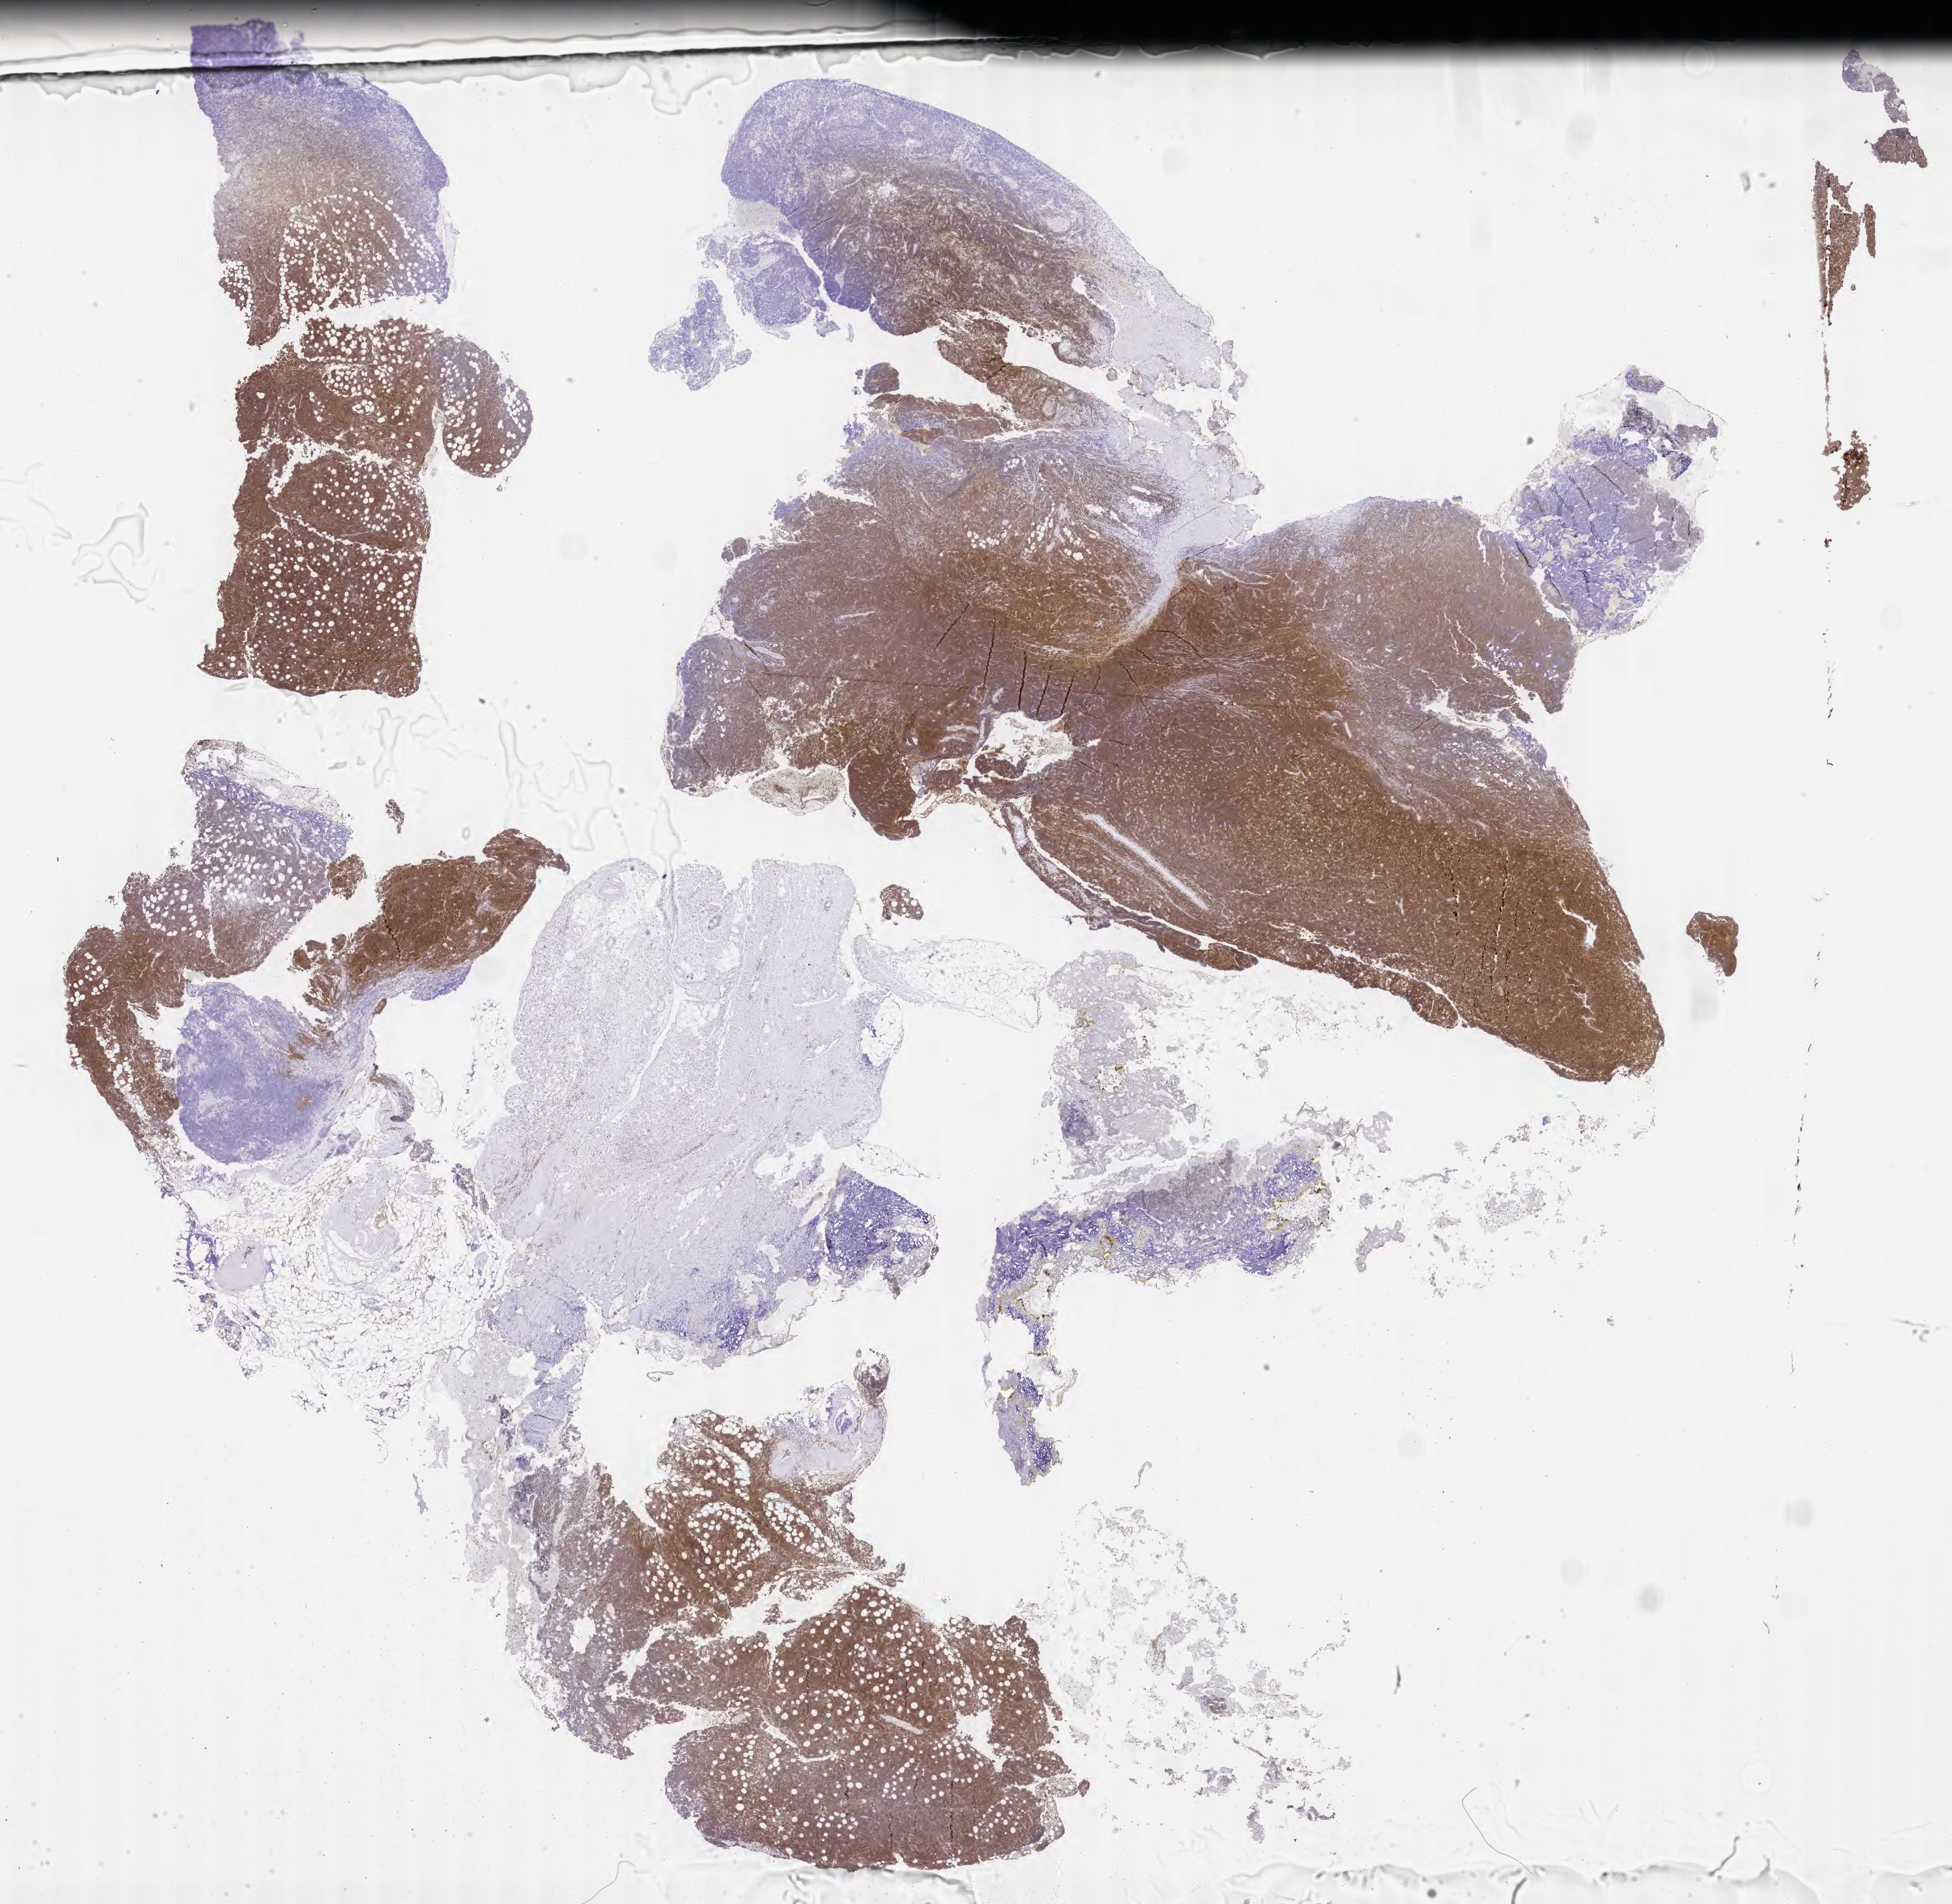
IHC for CD10, whole-slide image — a low-resolution overview of the entire scanned area, about 24.2 x 23.6 mm. Tumor tissue. Patient: female, age 72 years.
Histologic diagnosis: Burkitt lymphoma, NOS.